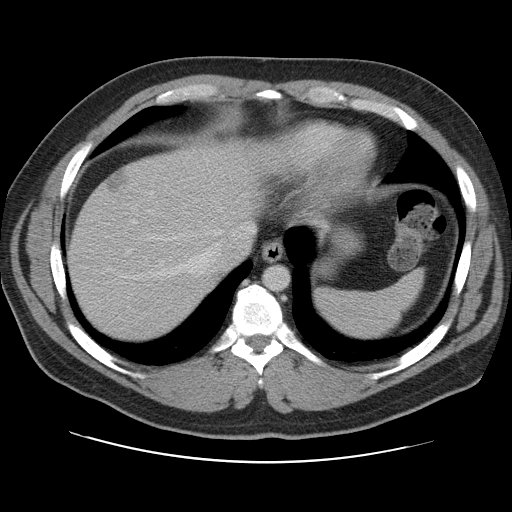
Contrast-enhanced abdominal CT, one axial slice; slice 93 of 109 in the series (ordered by position); soft-tissue window (W 400 / L 40 HU); 5 mm slice thickness; 512 × 512 image matrix, field of view 402 × 402 mm. Male patient, age 35 years. Case-level facts recorded for this patient, not image findings: diagnosis: colorectal cancer liver metastases, imaged before liver resection.
Annotated regions visible in this slice (expert manual segmentation):
- hepatic veins: box from (x=137, y=208) to (x=254, y=279) px
- liver: (x=69, y=140)–(x=268, y=341)
- planned liver remnant (the part of the liver to remain after resection): (x=70, y=140)–(x=268, y=341)
- liver metastasis: (x=107, y=171)–(x=129, y=192)